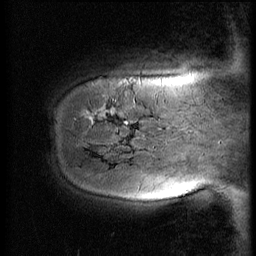
Breast MRI (dynamic contrast-enhanced), one sagittal slice. Position 8 of 56 along the scan axis. 3 images stored at this slice position (order not interpretable as contrast timing). 1.5 T. TE 4.2 ms, TR 9 ms. 2.5 mm slice thickness. 256 × 256 image matrix. Patient: female, 51 years. From the clinical record (not read from this slice): setting: breast cancer imaged before/during neoadjuvant chemotherapy; receptor status: HR-positive, HER2-negative.
Annotated regions visible in this slice (semi-automatically segmented with operator editing):
- analysis volume of interest (the breast-tissue region the enhancement analysis was run in; not a lesion): bounding box [x1, y1, x2, y2] px = [46, 58, 167, 161]
- tumour enhancement mask (voxels above the 140 % enhancement threshold inside the analysis volume of interest): [98, 110, 113, 119]